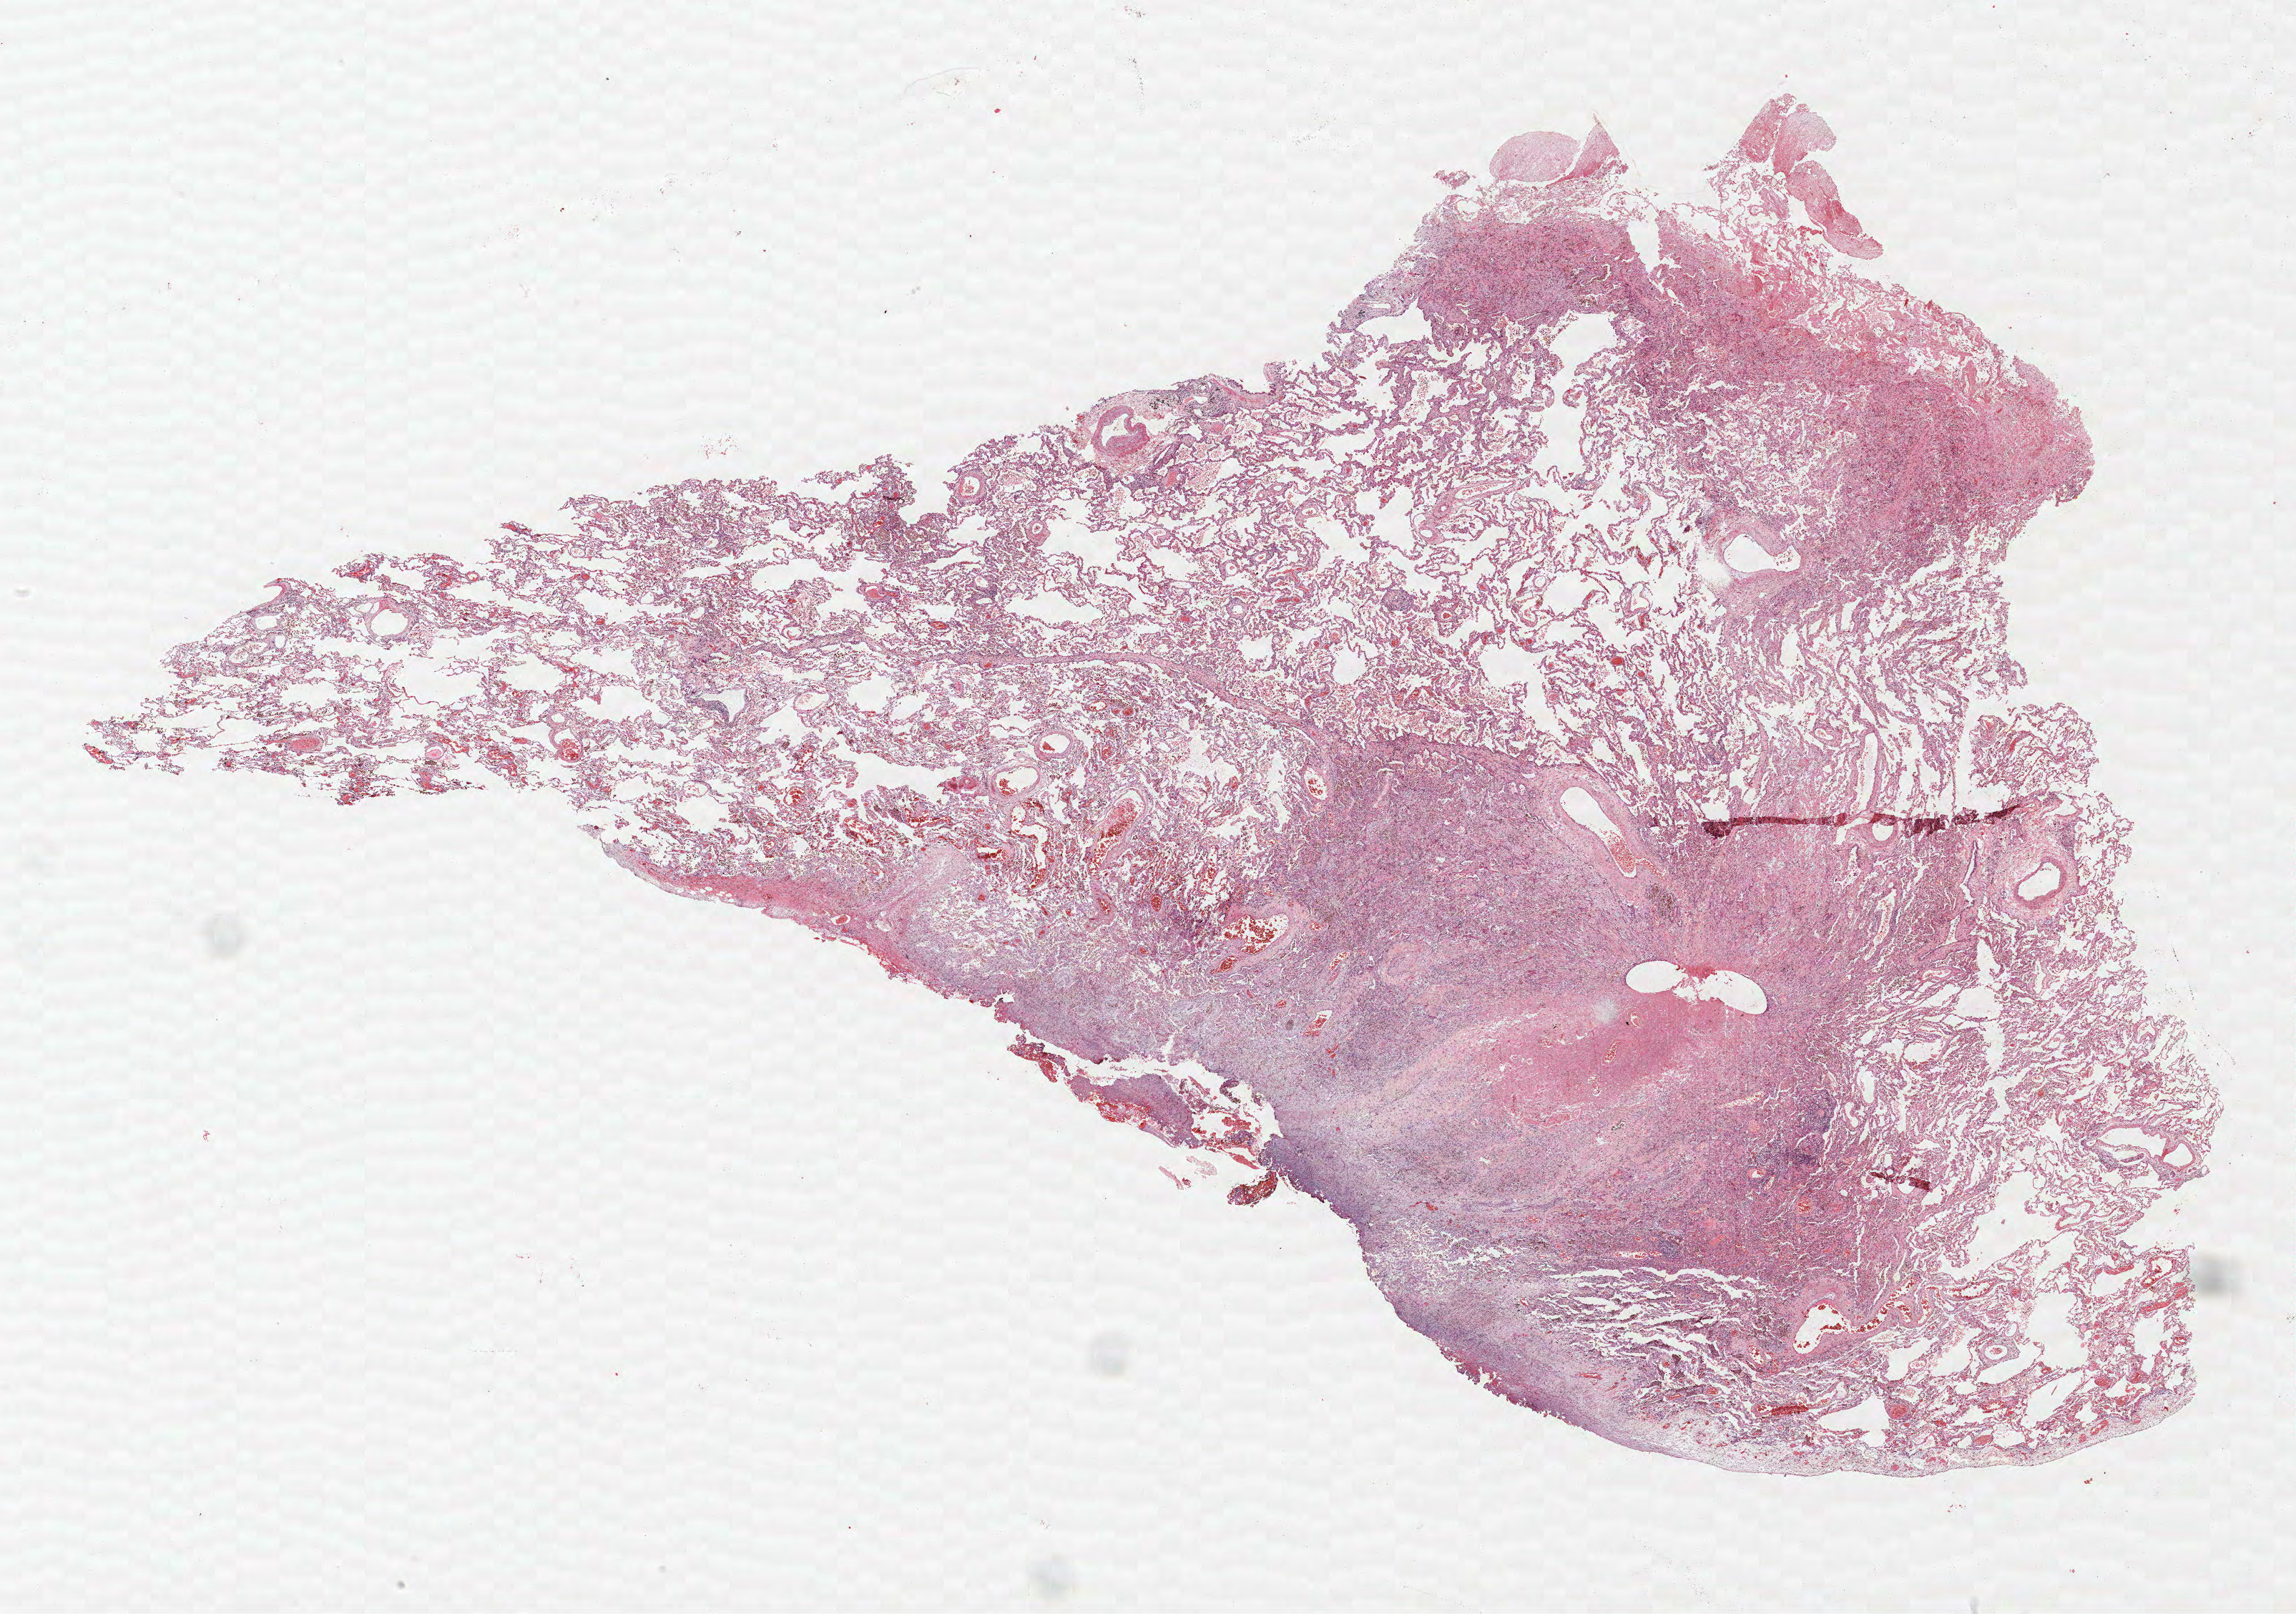
H&E-stained whole-slide image, shown as a low-resolution overview of the whole scanned area (about 25.7 x 18.1 mm, from a 40x scan), FFPE section, lung. Male, age 64 at enrolment. Former smoker at enrolment. Grade: poorly differentiated (G3).
Stage (AJCC 6th edition): IA. Participant's lung-cancer diagnosis: Adenocarcinoma, NOS. Primary tumour location (clinical record): left upper lobe. Tumour size (pathology): 10 mm.